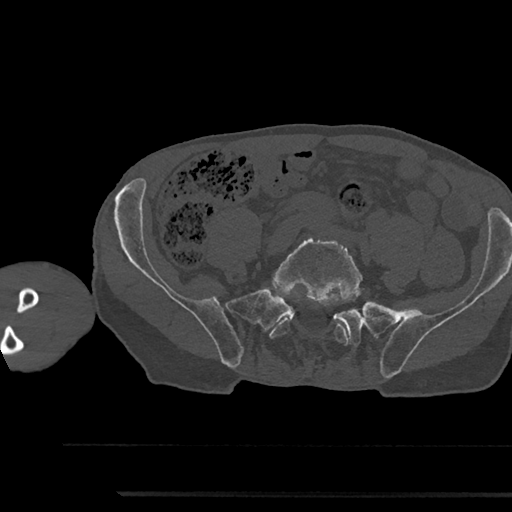
CT including the spine, one axial slice. Position 321 of 797 along the scan axis. Reconstruction kernel Br40s/3. 120 kVp. Bone window (W 1800 / L 400 HU). 0.5 mm slice thickness. 512 × 512 image matrix, field of view 367 × 367 mm. Patient: male, 79 years. From the clinical record (not read from this slice): primary cancer: prostate.
Outlined on this slice (semi-automatically segmented with operator editing):
- L5 vertebra: bounding box (x1, y1, x2, y2) in pixels: (269, 234, 362, 344)